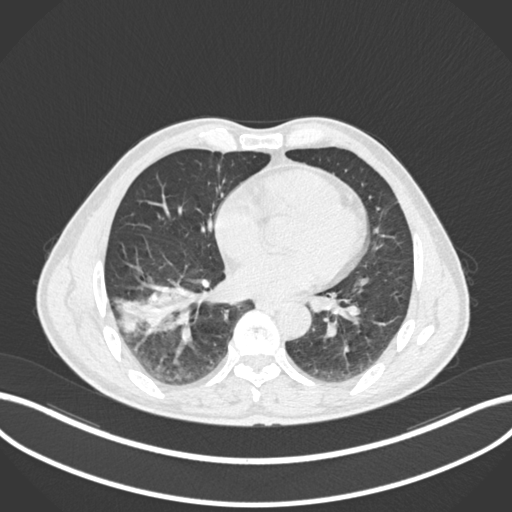
Chest CT, one axial slice; slice 75 of 208 in the series (ordered by position); reconstruction kernel B30f; 120 kVp; lung window (W 1500 / L -600 HU); 1 mm slice thickness; 512 × 512 image matrix. Patient: male, 58 years. From the clinical record (not read from this slice): clinical TNM (as recorded): T3 N0 M0.
Structures marked on this image (rectangle marked by the reading radiologist):
- lung tumour (recorded histology: squamous cell carcinoma): box from (x=110, y=281) to (x=198, y=336) px